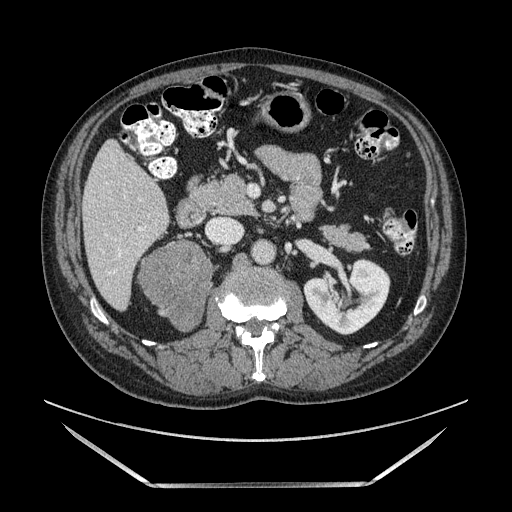
Contrast-enhanced abdominal CT, one axial slice; slice 58 of 185 in the series (ordered by position); soft-tissue window (W 400 / L 40 HU); 1.25 mm slice thickness; 512 × 512 image matrix, field of view 440 × 440 mm. Male patient. From the clinical record (not read from this slice): diagnosis: adrenocortical carcinoma; tumour side: right adrenal; tumour size at pathology: 10.3 cm; Ki-67 index: 20 %; stage (as recorded): 3.
Outlined on this slice (semi-automatically segmented with operator editing):
- mass: box from (x=140, y=243) to (x=210, y=329) px